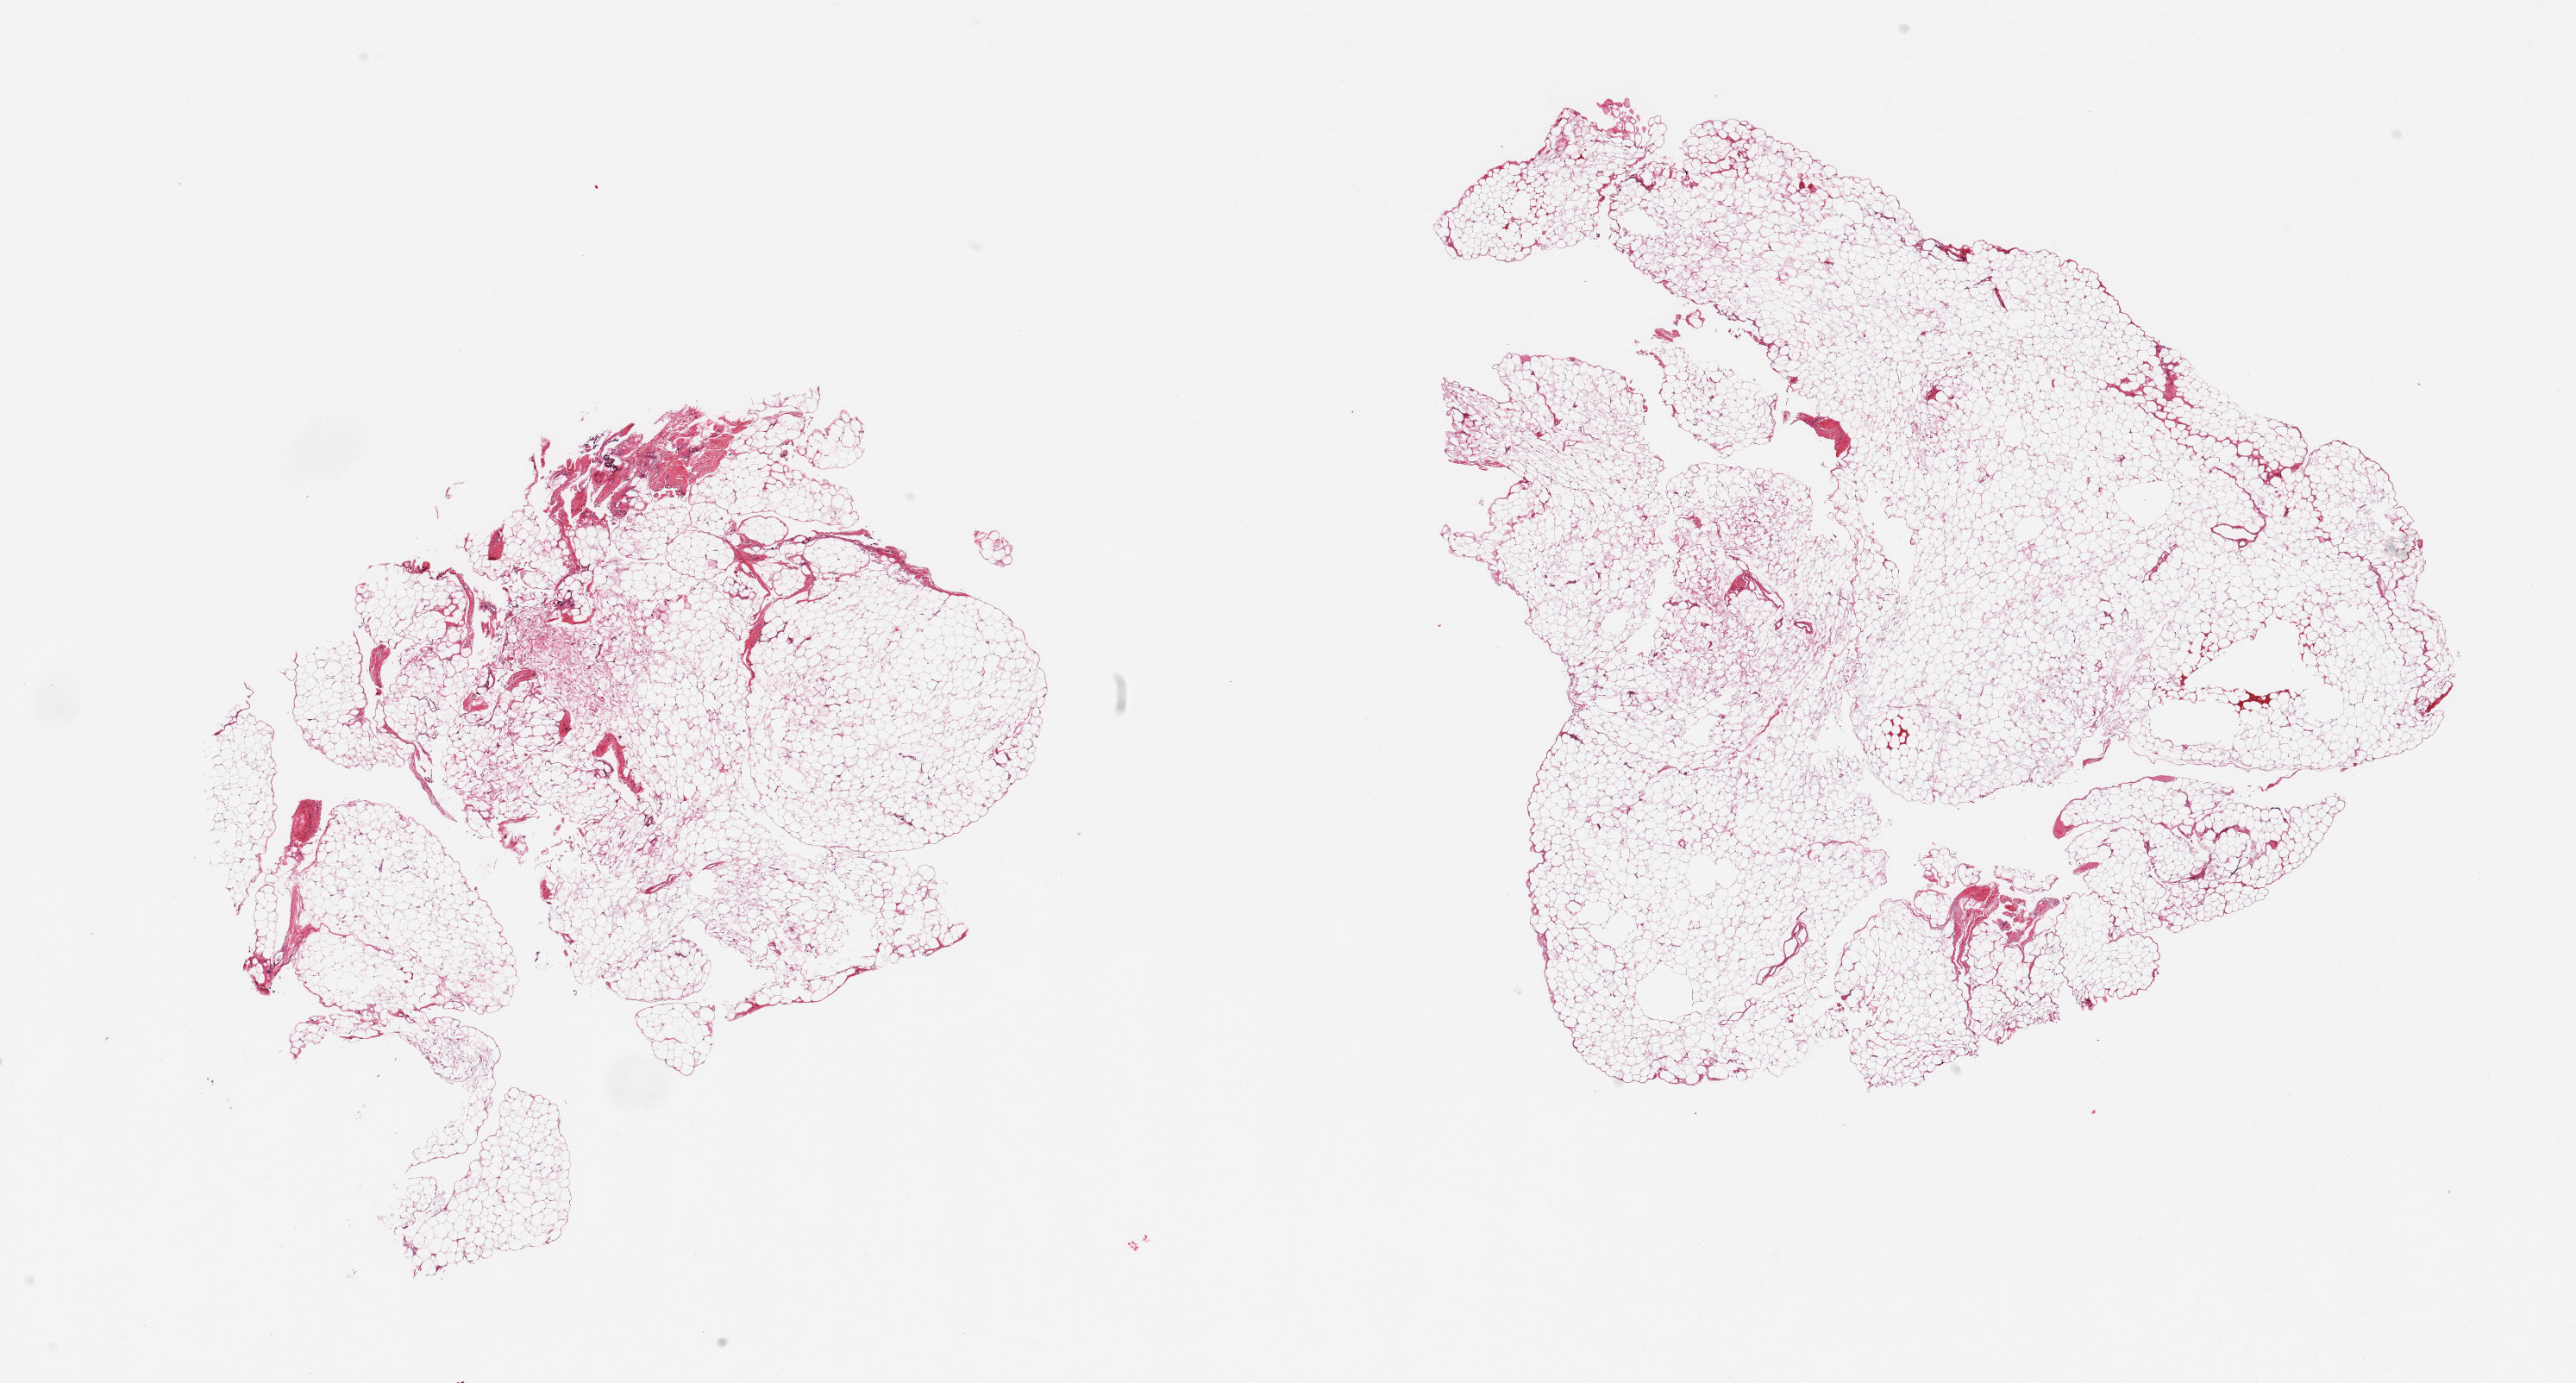
Whole-slide image, H&E stain — whole scanned area (about 23.6 x 12.7 mm, acquisition: 20x scan) shown as a low-resolution overview. Male donor.
* specimen: PAXgene-fixed paraffin-embedded (PFPE) section; sampled site (target tissue): omentum; donor tissue sample